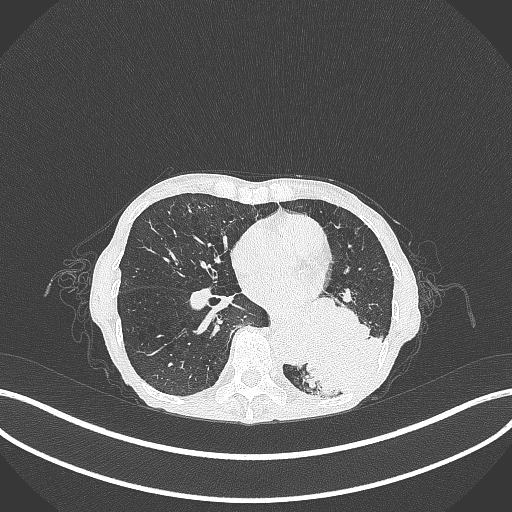
Chest CT, one axial slice; position 117 of 347 along the scan axis; 120 kVp; lung window (W 1500 / L -600 HU); 512 × 512 image matrix. Patient: female, 70 years. Case-level facts recorded for this patient, not image findings: clinical TNM (as recorded): T3 N0 M0.
Structures marked on this image (bounding box drawn by a radiologist):
- lung tumour (recorded histology: small cell carcinoma): bounding box (x1, y1, x2, y2) in pixels: (294, 307, 390, 398)